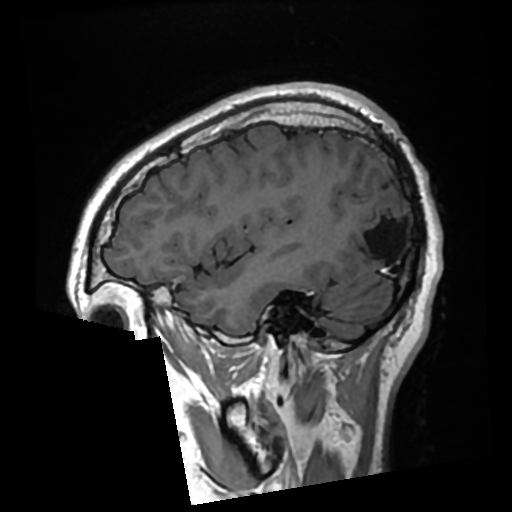
Brain MRI from a brain-tumour surgery series, one sagittal slice. Position 80 of 276 along the scan axis. T1-weighted post-contrast. 0.7 mm slice thickness. 512 × 512 image matrix. From the clinical record (not read from this slice): histopathology: Glioma with ependymal features; WHO grade: 2.
Structures marked on this image (outlined manually by an expert reader):
- previous resection cavity: bounding box [x1, y1, x2, y2] px = [350, 218, 400, 263]